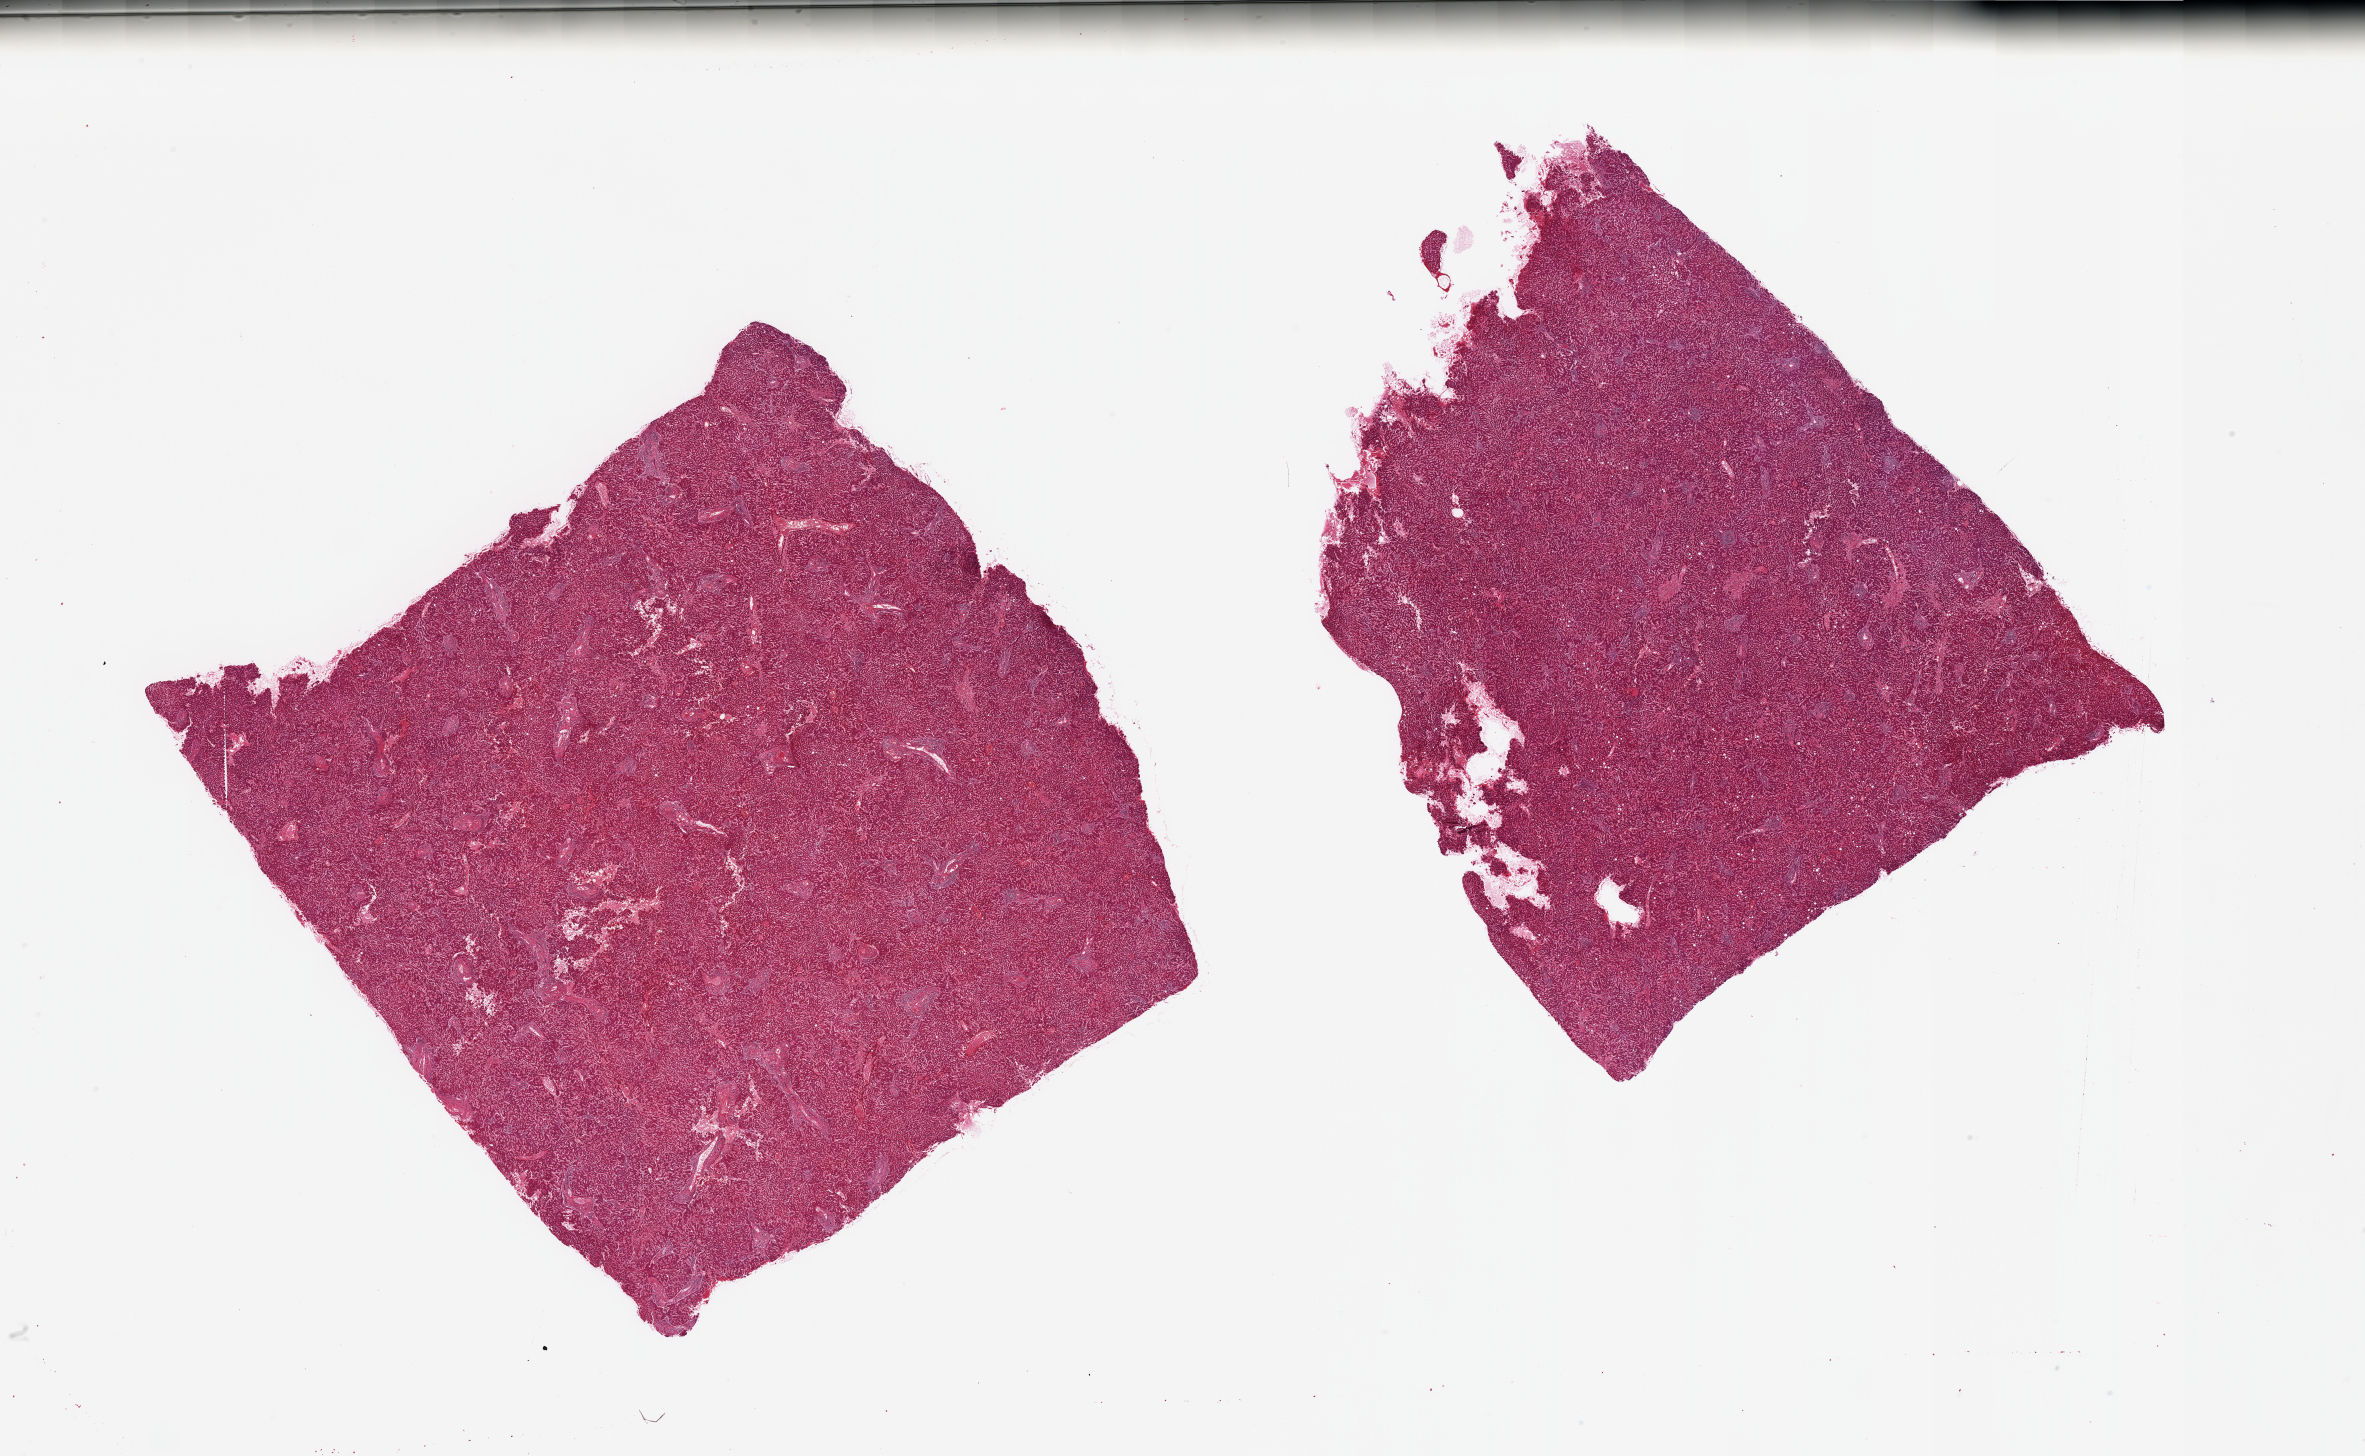
Digitized hematoxylin and eosin (H&E)-stained section, brightfield — shown as a low-resolution overview of the whole scanned area (about 37.4 x 23.0 mm, slide scanned at 20x), PAXgene-fixed paraffin-embedded (PFPE) section, sampled site (target tissue): liver, donor tissue sample. Donor sex: male.
• reviewer comment on this tissue sample: 2 pieces; moderate increase in portal tract lymphocytes